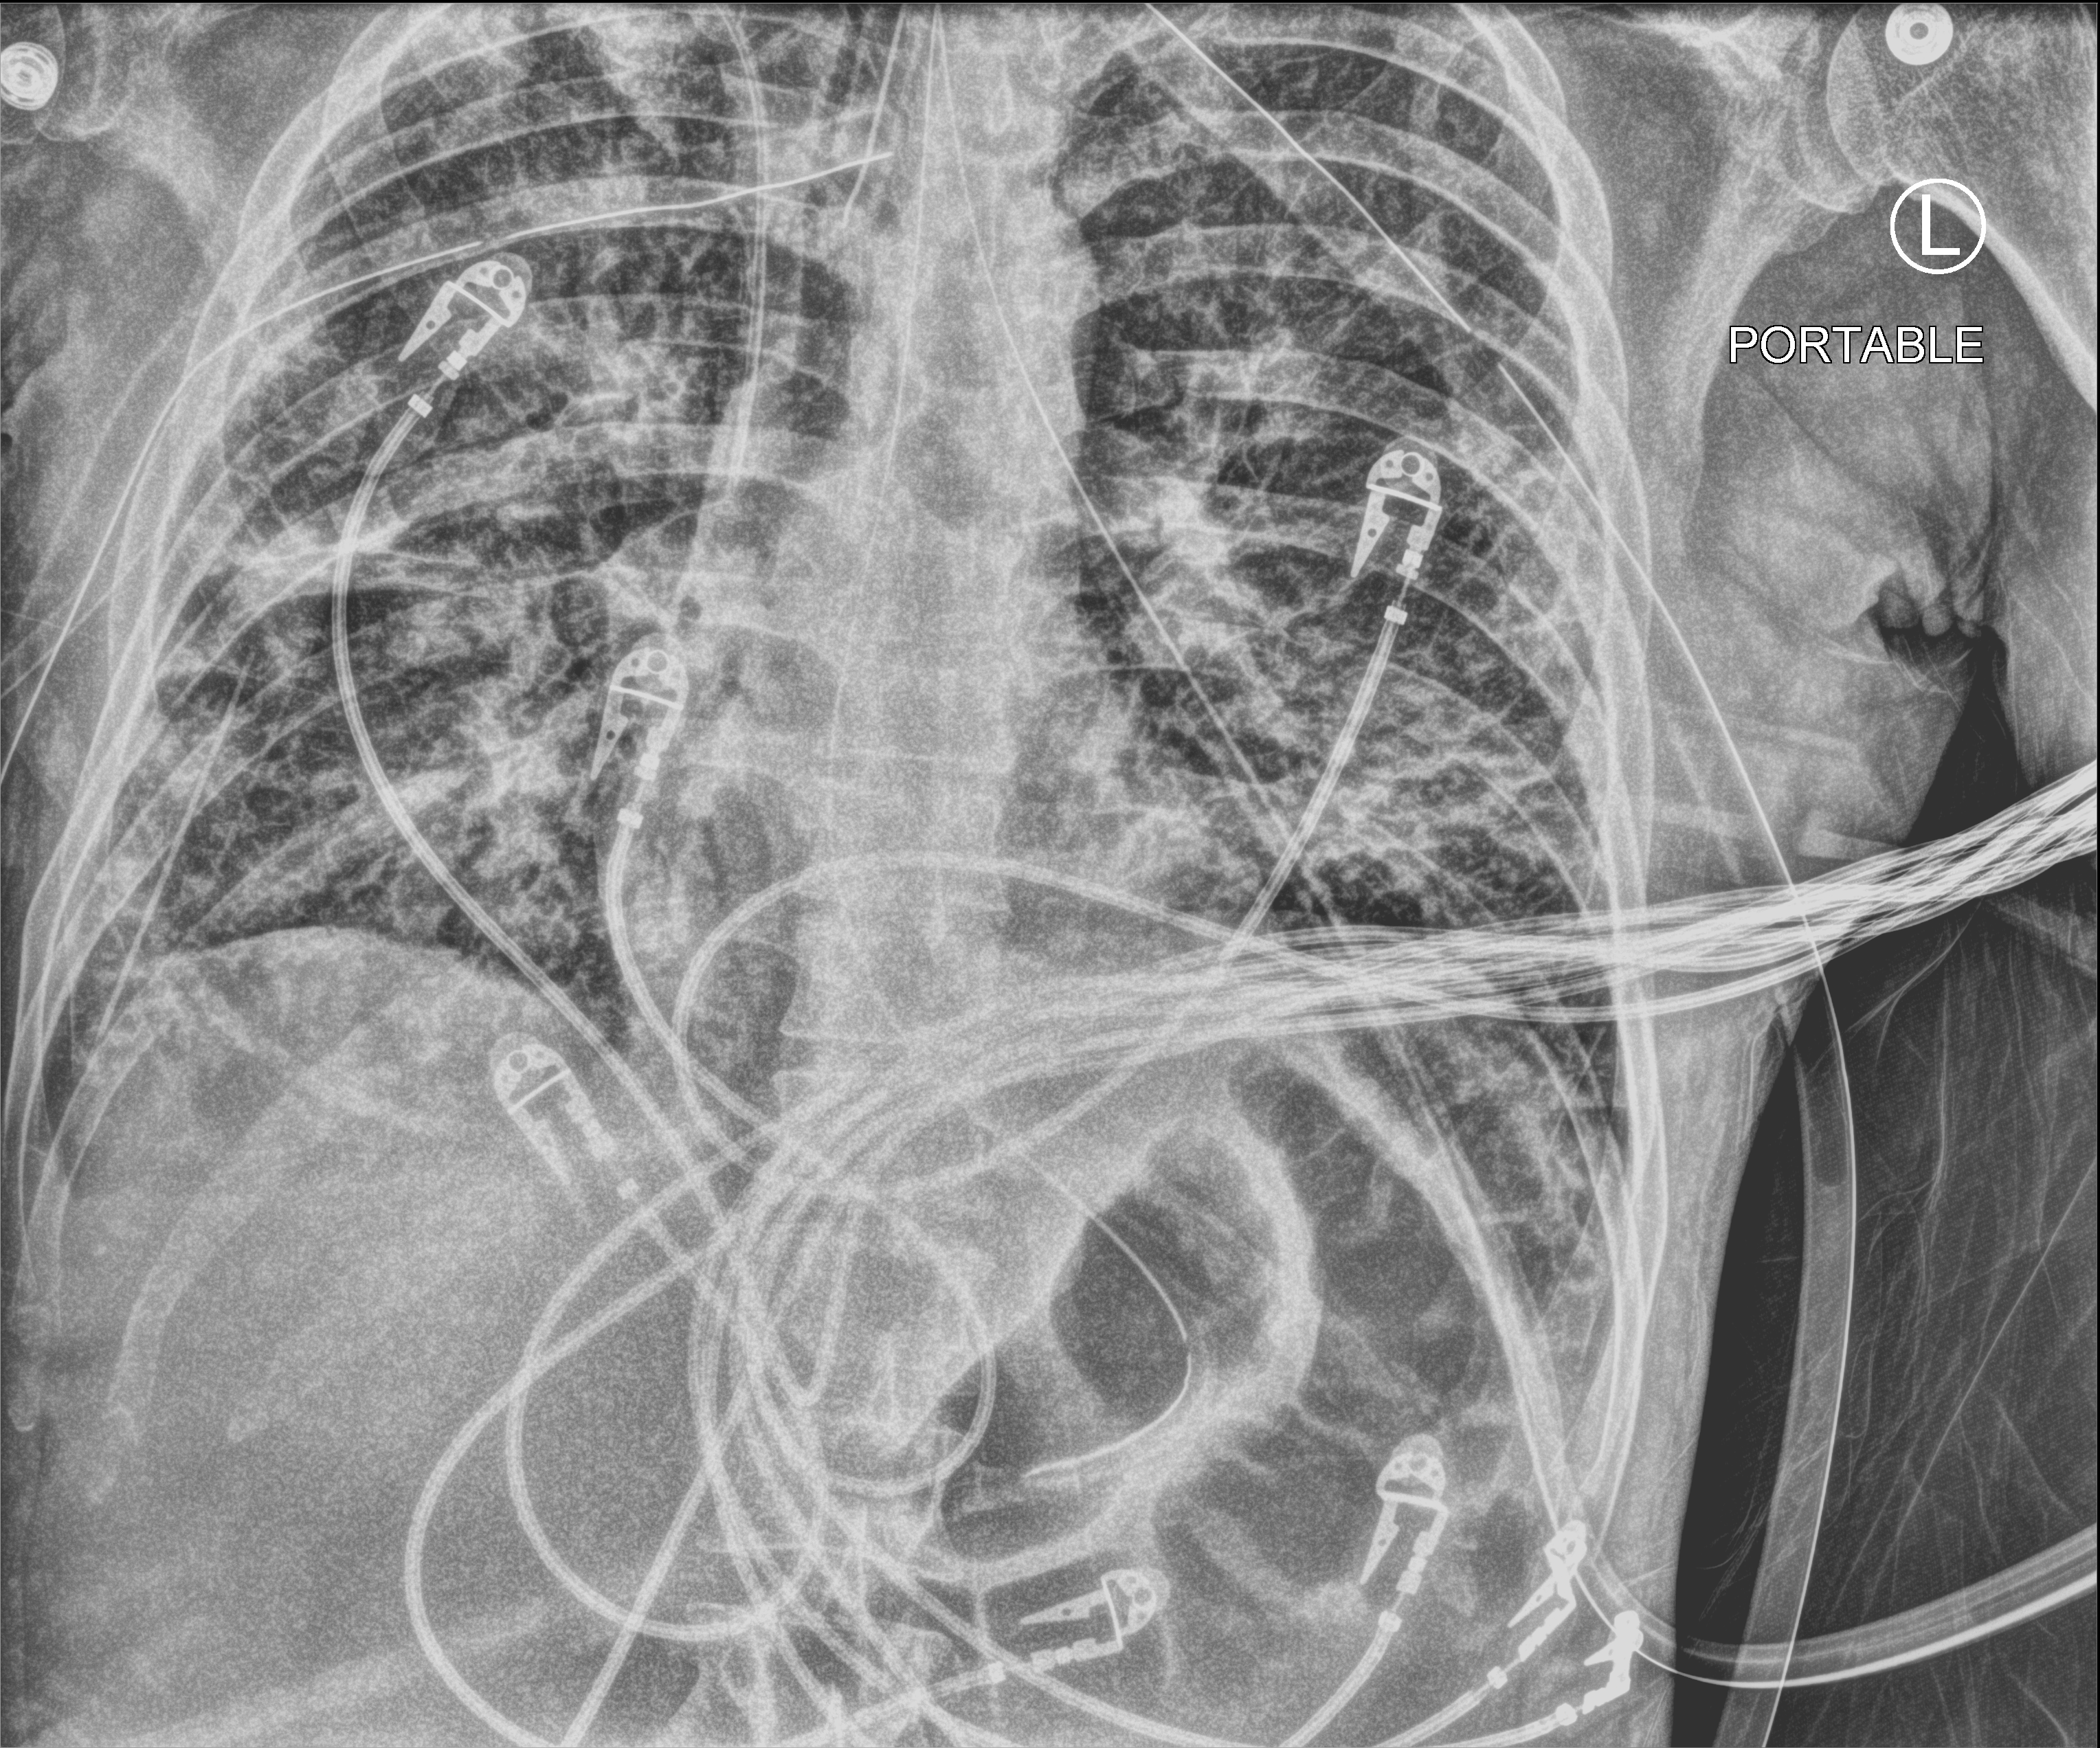
Bedside chest radiograph (computed radiography), anteroposterior (AP) projection. Male patient hospitalised with COVID-19, age 18–59 years.
Hospital-stay facts (about this admission, not read from this image; timing relative to this image not recorded): COPD (admission record): no.